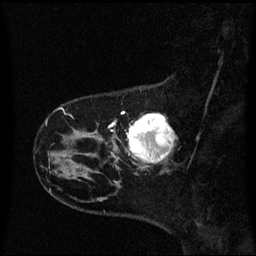
Breast MRI (dynamic contrast-enhanced), one sagittal slice. Dynamic contrast-enhanced series, image 2 of 3 at this slice position (ordered by acquisition). 1.5 T. TE 4.2 ms, TR 8.4 ms. 2 mm slice thickness. 256 × 256 image matrix, field of view 220 × 220 mm. Patient: female, 41 years. From the clinical record (not read from this slice): setting: breast cancer imaged before/during neoadjuvant chemotherapy; receptor status: triple-negative.
Structures marked on this image (semi-automatically segmented with operator editing):
- analysis volume of interest (the breast-tissue region the enhancement analysis was run in; not a lesion): bounding box <116,114,175,169> (left, top, right, bottom; pixels)
- tumour enhancement mask (voxels above the 70 % enhancement threshold inside the analysis volume of interest): <127,114,174,163>